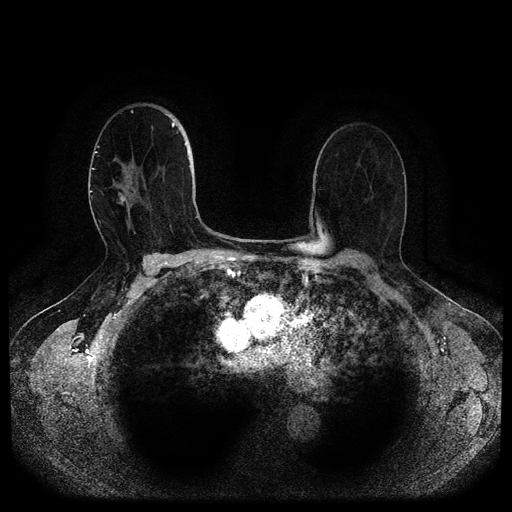
Breast MRI (dynamic contrast-enhanced, multi-phase), one axial slice; position 65 of 116 along the scan axis; dynamic contrast-enhanced series, time point 2 of 5 at this slice position (early post-contrast); 1.5 T; TE 2.6 ms, TR 5.3 ms; 2 mm slice thickness; 512 × 512 image matrix, field of view 350 × 350 mm. Female patient, age 82 years.
Annotated regions visible in this slice (semi-automatically segmented with operator editing):
- breast lesion (labelled 'tumour' in the annotation; benign lesions carry a separate 'benign' label): bounding box (x1, y1, x2, y2) in pixels: (118, 192, 128, 205)